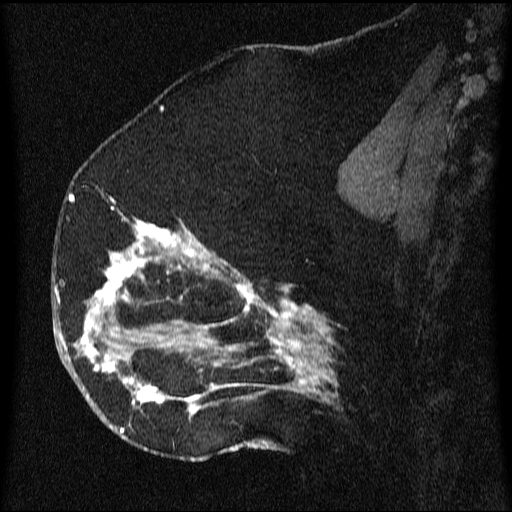
Breast MRI (dynamic contrast-enhanced), one sagittal slice. Position 34 of 64 along the scan axis. Dynamic contrast-enhanced series, image 2 of 3 at this slice position (ordered by acquisition). 1.5 T. TE 4.2 ms, TR 9.1 ms. 512 × 512 image matrix, field of view 180 × 180 mm. Female patient, age 52 years.
Structures marked on this image (semi-automatically segmented with operator editing):
- analysis volume of interest (the breast-tissue region the enhancement analysis was run in; not a lesion): bounding box (x1, y1, x2, y2) in pixels: (61, 203, 339, 438)
- tumour enhancement mask (voxels above the 70 % enhancement threshold inside the analysis volume of interest): (62, 209, 338, 438)